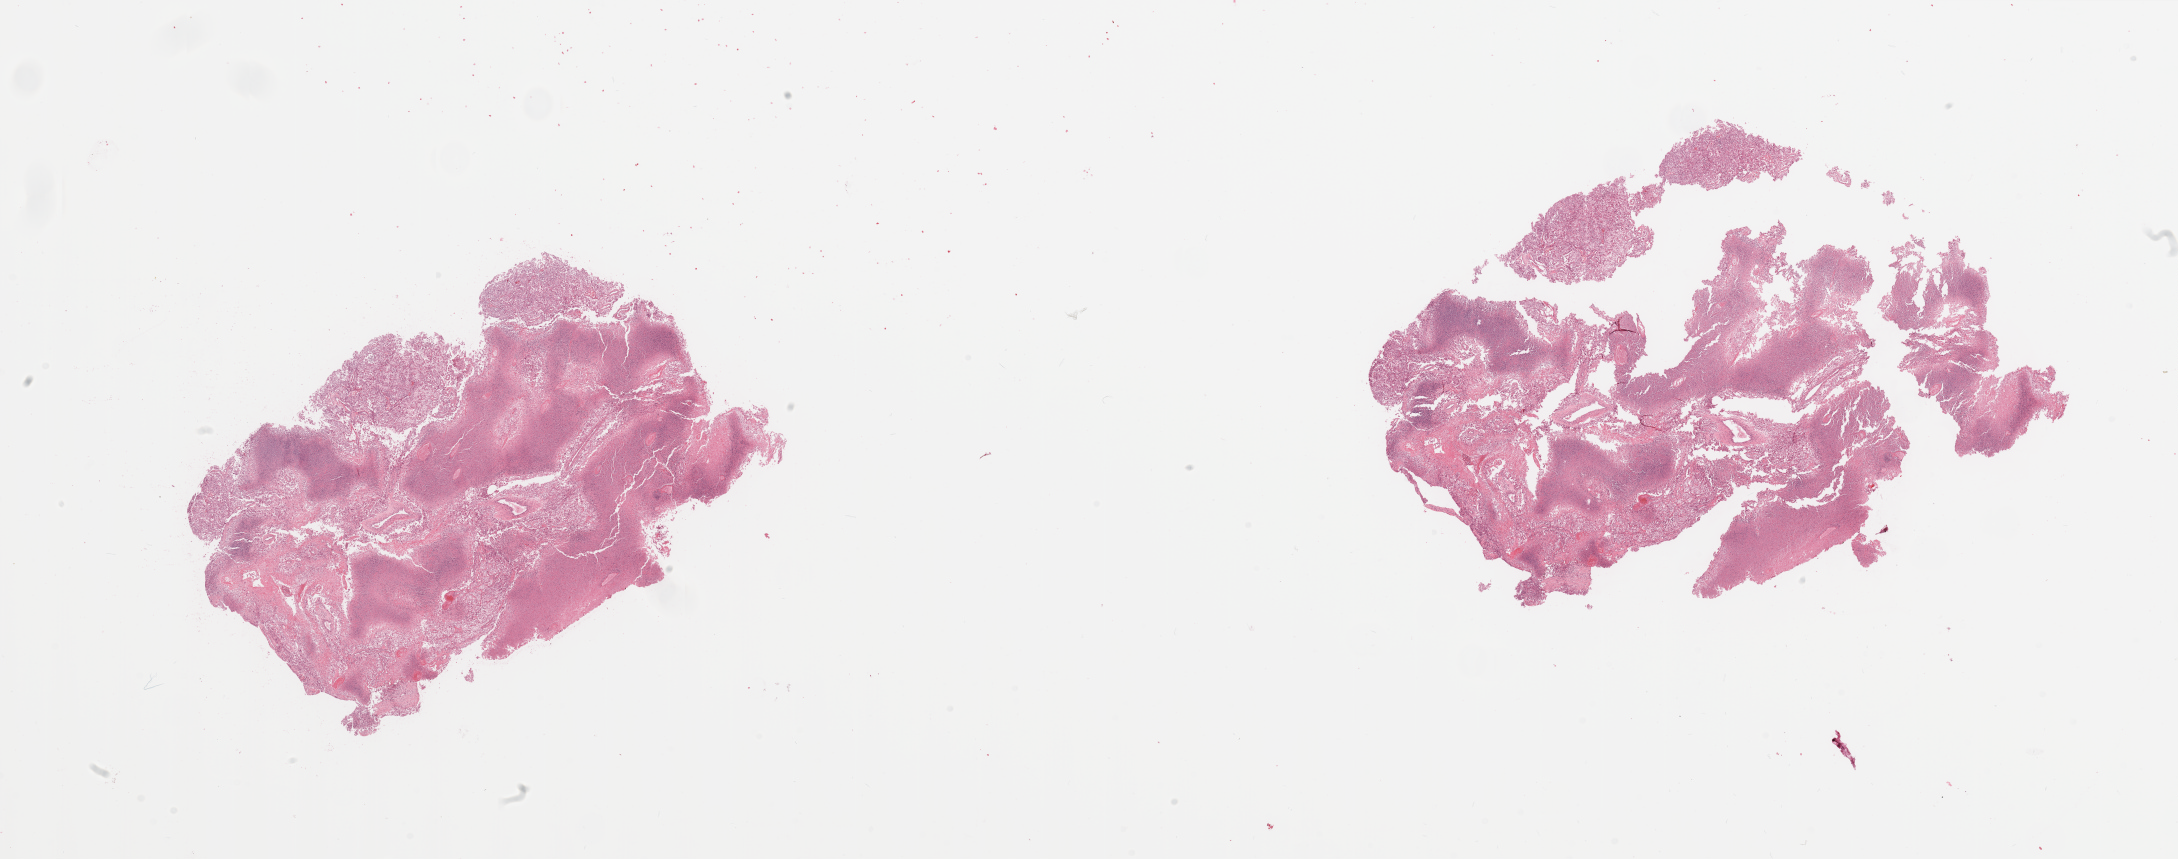
Digitized H&E tissue section (whole slide) — shown as a low-resolution overview of the whole scanned area (about 34.5 x 13.6 mm, from a 20x scan); tumour tissue sample, kidney. Patient: male, age 57 years.
Diagnosis: Renal cell carcinoma, NOS.